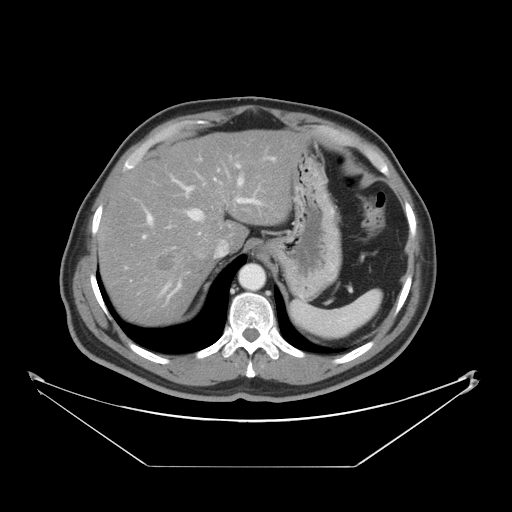
Contrast-enhanced abdominal CT, one axial slice; slice 34 of 46 in the series (ordered by position); reconstruction kernel STANDARD; 120 kVp; intravenous contrast given; soft-tissue window (W 400 / L 40 HU); 5 mm slice thickness; 512 × 512 image matrix. Male patient, age 57 years. Case-level facts recorded for this patient, not image findings: diagnosis: colorectal cancer liver metastases, imaged before liver resection; multiple liver metastases: no; largest metastasis: 3.3 cm; disease in both lobes: no.
Structures marked on this image (expert manual segmentation):
- hepatic veins: box from (x=185, y=208) to (x=203, y=221) px
- liver: (x=99, y=132)–(x=304, y=323)
- planned liver remnant (the part of the liver to remain after resection): (x=99, y=132)–(x=304, y=320)
- portal vein (with intrahepatic branches): (x=142, y=164)–(x=261, y=301)
- liver metastasis: (x=154, y=249)–(x=178, y=274)